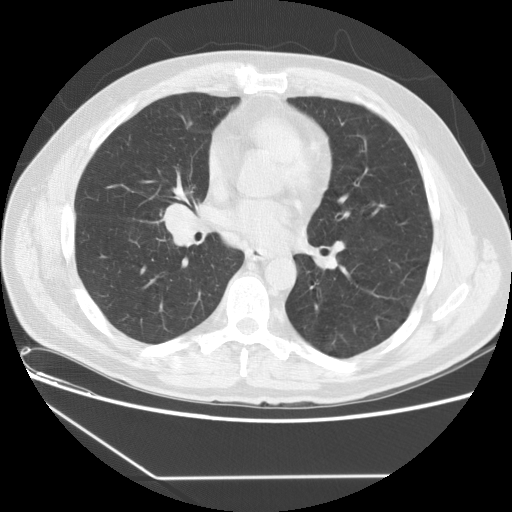
Low-dose screening chest CT, one axial slice. Position 73 of 154 along the scan axis. 120 kVp. Lung window (W 1500 / L -600 HU). 2.5 mm slice thickness. 512 × 512 image matrix, field of view 370 × 370 mm.
Structures marked on this image (manually delineated by an expert):
- lesion 1 (tumor, middle lobe of right lung): bounding box <166,204,198,235> (left, top, right, bottom; pixels)